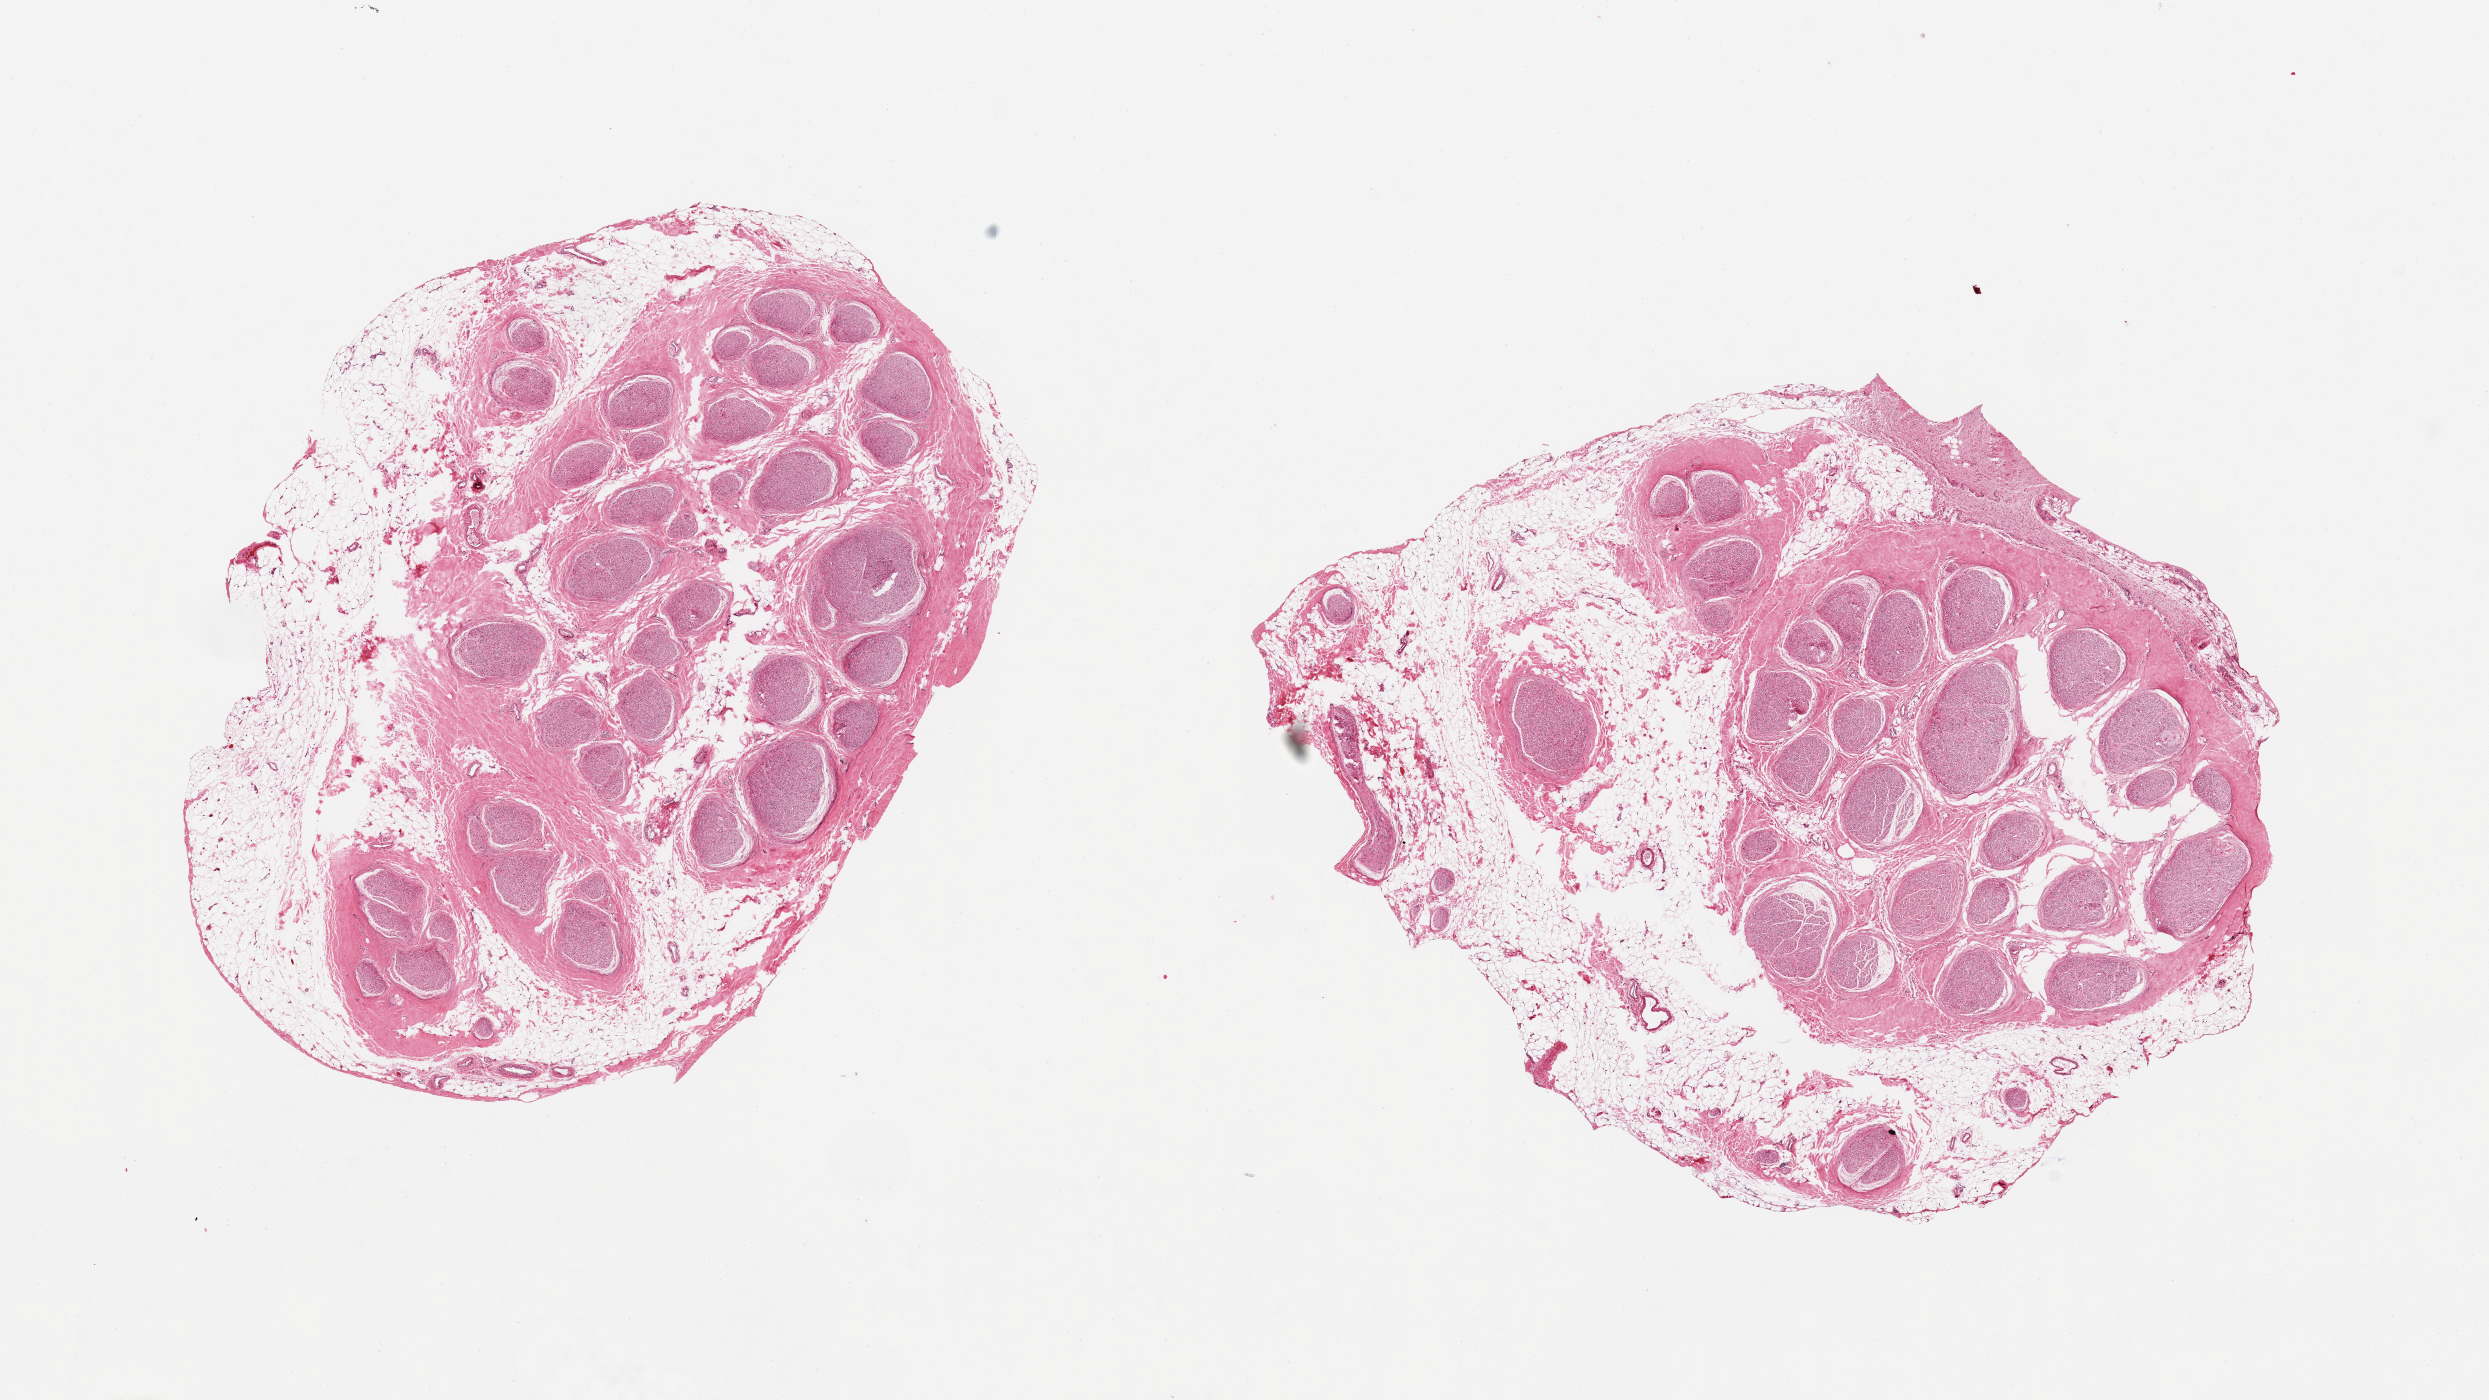
Haematoxylin and eosin whole-slide image, a low-resolution overview of the entire scanned area, about 19.7 x 11.1 mm, PAXgene-fixed, paraffin-embedded tissue, target tissue: tibial nerve, donor tissue sample.
Review note (as recorded): 2 piece, 7x5 & 7x6 mm;40-50% adipose tiissue.